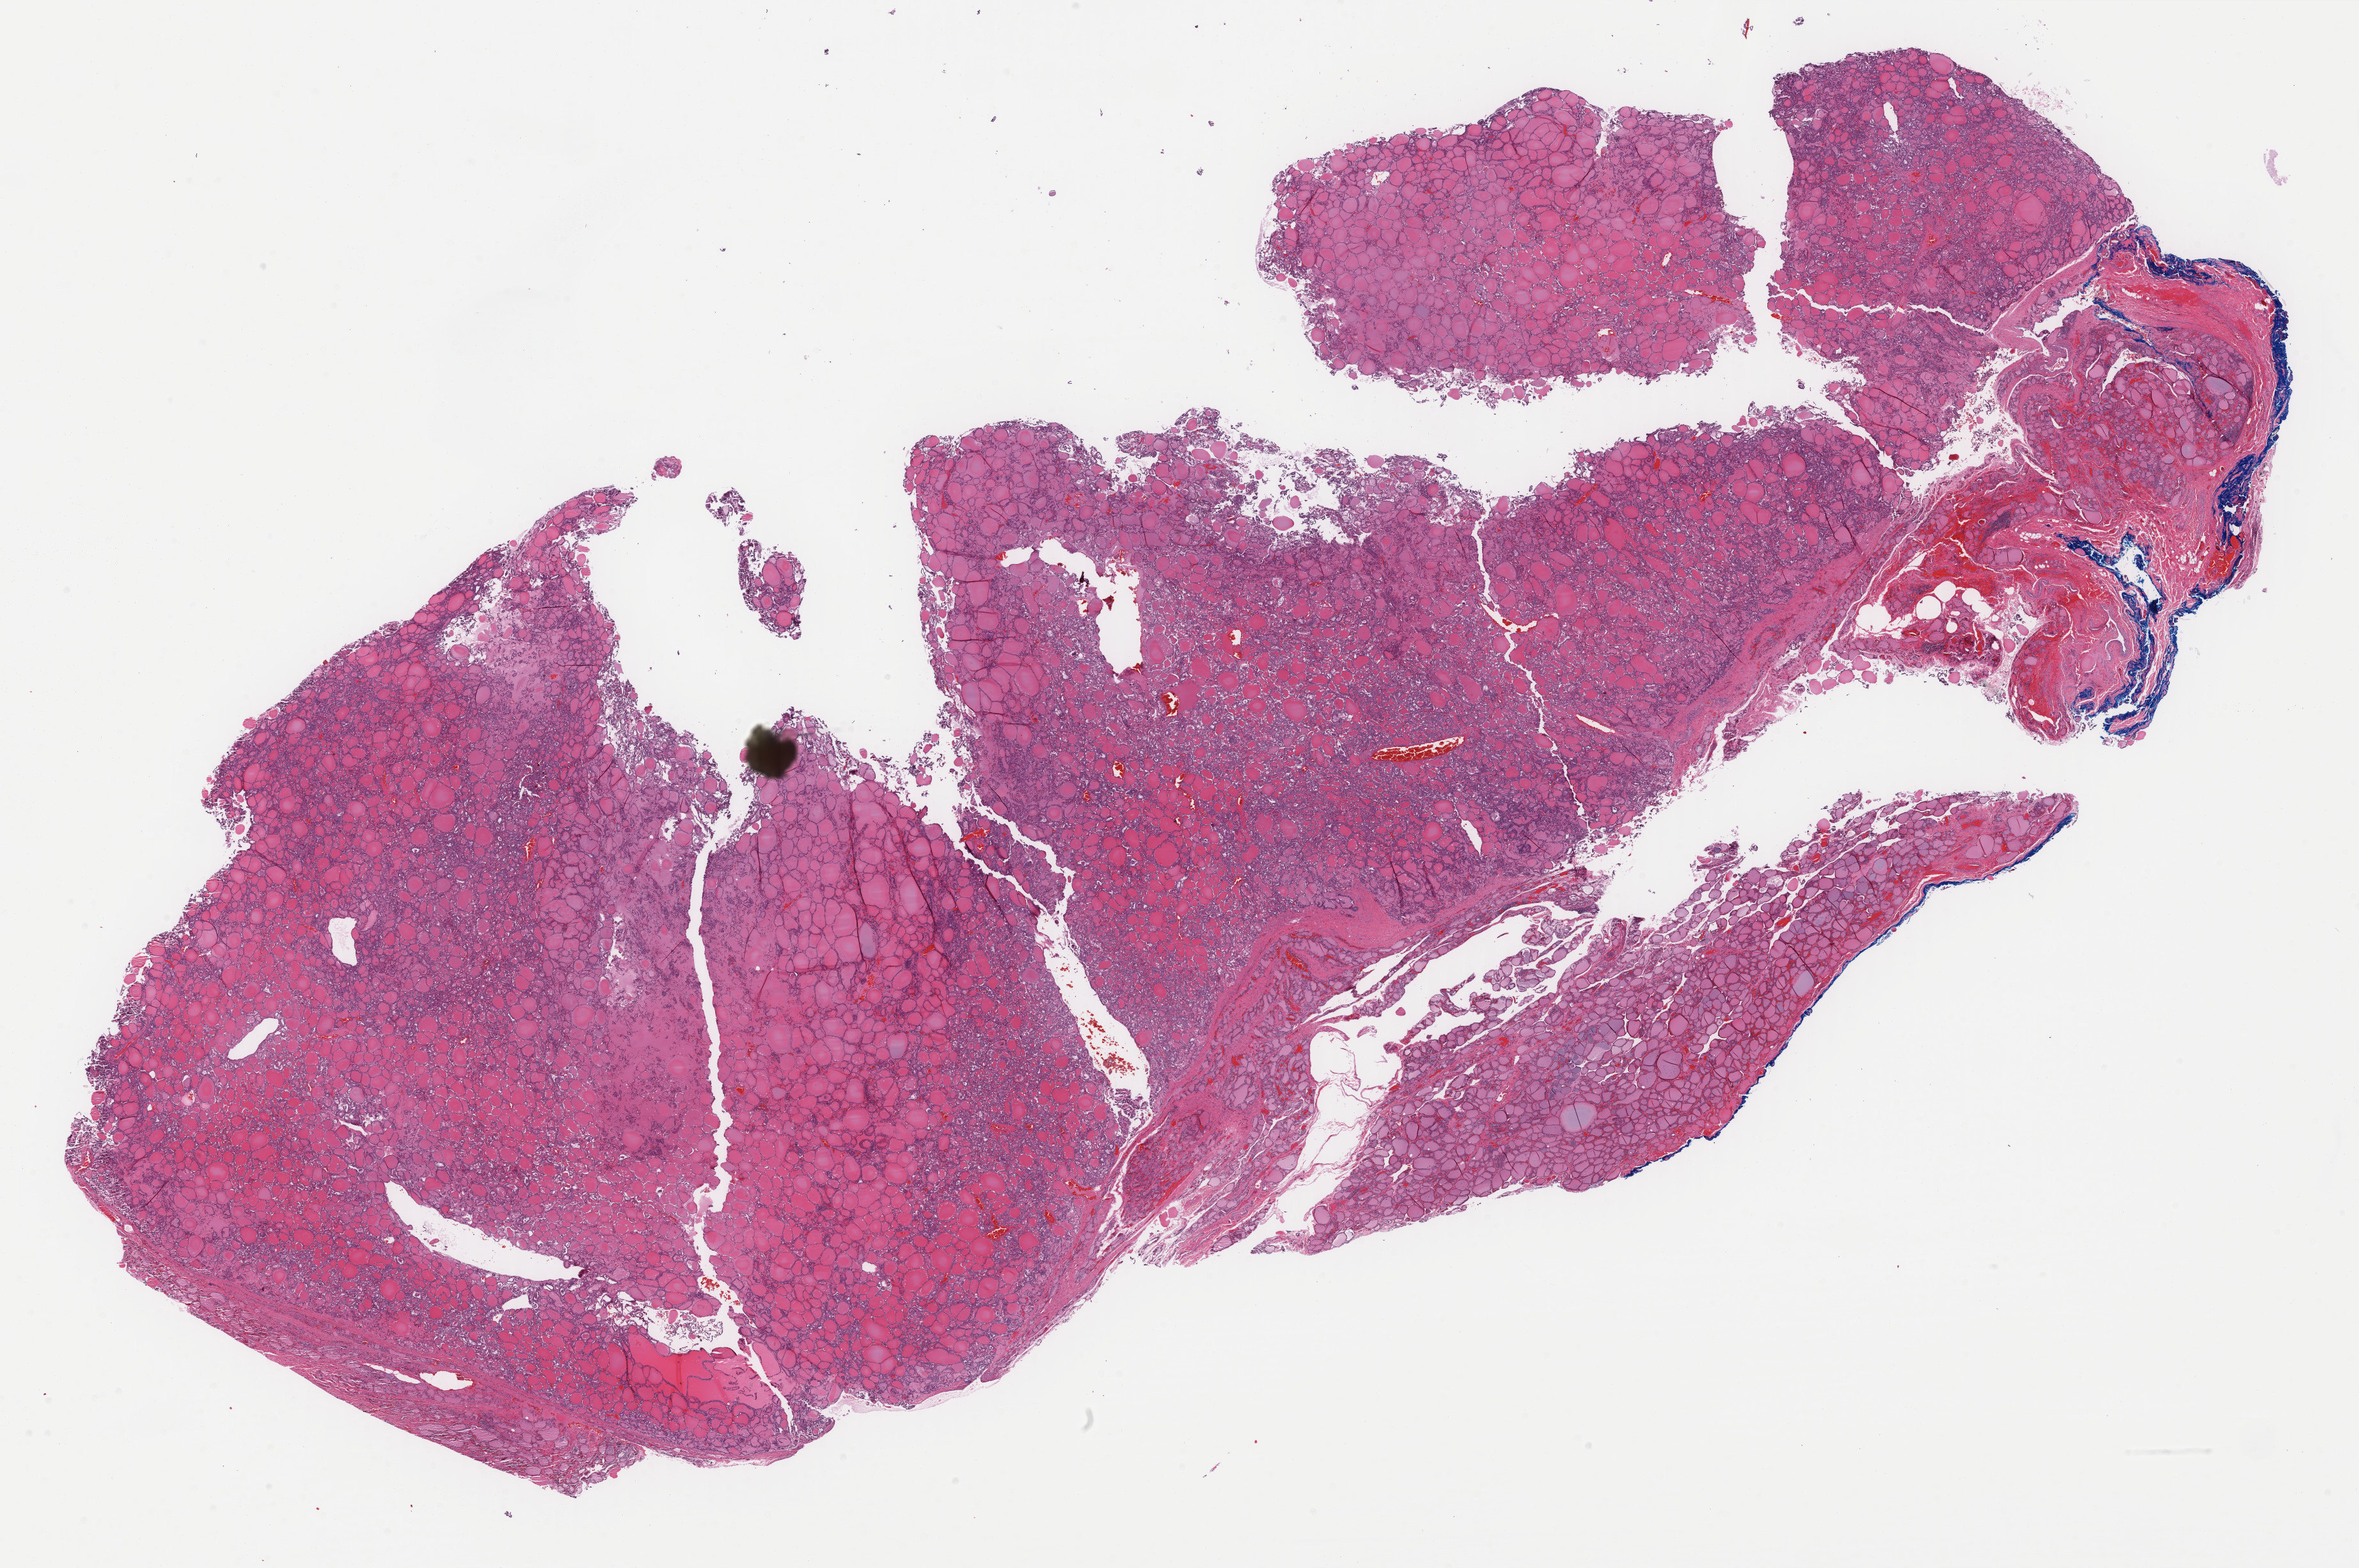
Whole-slide histology image, Hematoxylin and eosin (H&E) stained, whole scanned area (about 29.3 x 19.5 mm, acquisition: 40x scan) shown as a low-resolution overview; FFPE section; sample: primary tumour, thyroid. Patient: female, age at initial diagnosis 51 years.
* lymph nodes positive (case pathology): 0 of 1 examined
* pathologic diagnosis: Papillary carcinoma, follicular variant
* AJCC pathologic stage: III (7th edition)